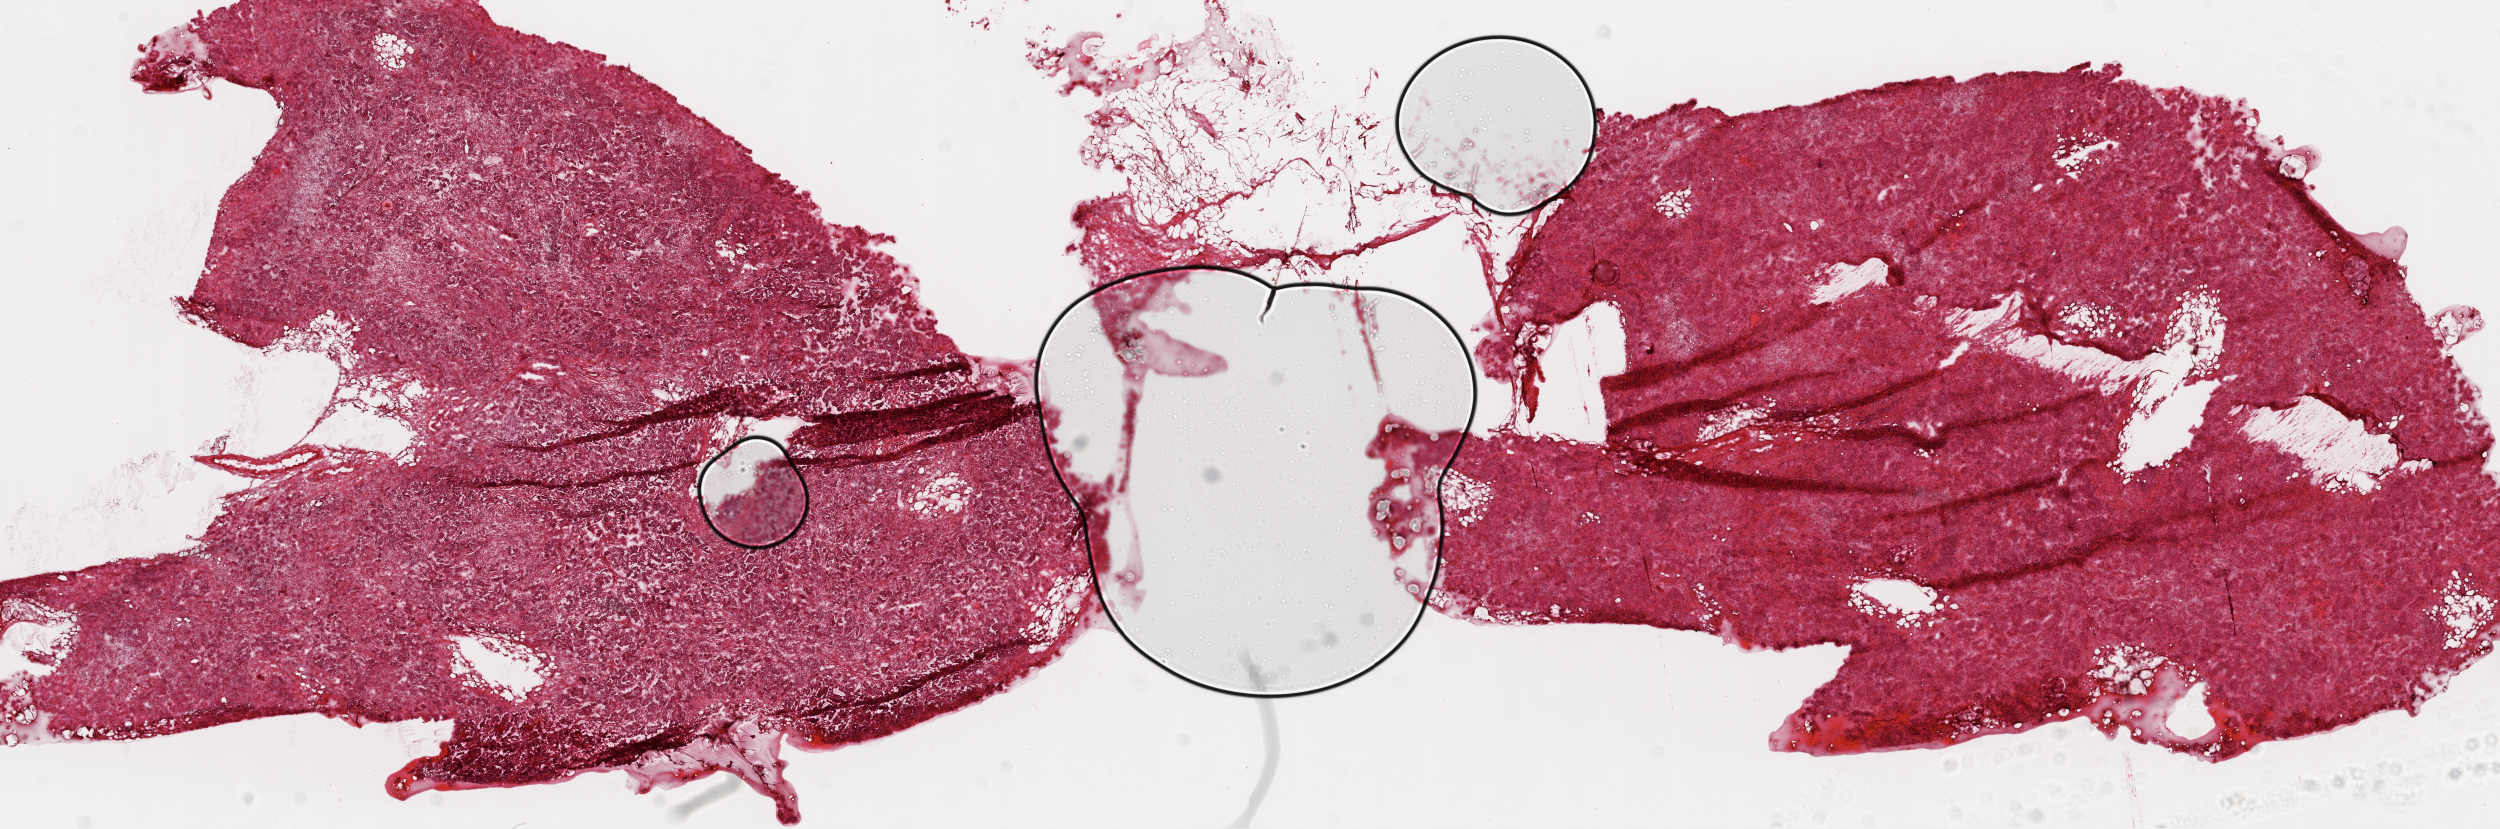
Whole-slide histology image, H&E, whole scanned area (about 20.1 x 6.7 mm) shown as a low-resolution overview. Frozen section from the top of the tissue portion. Ovary, primary tumour sample. Female, age 58 years at initial diagnosis. Histologic grade: G3 (poorly differentiated). Slide review estimates, as recorded: tumour cells 79%, tumour nuclei 80%, normal cells 0%, stromal cells 20%, necrosis 1%.
Laterality: bilateral. FIGO stage: IIIC. Pathologic diagnosis: Serous cystadenocarcinoma, NOS.